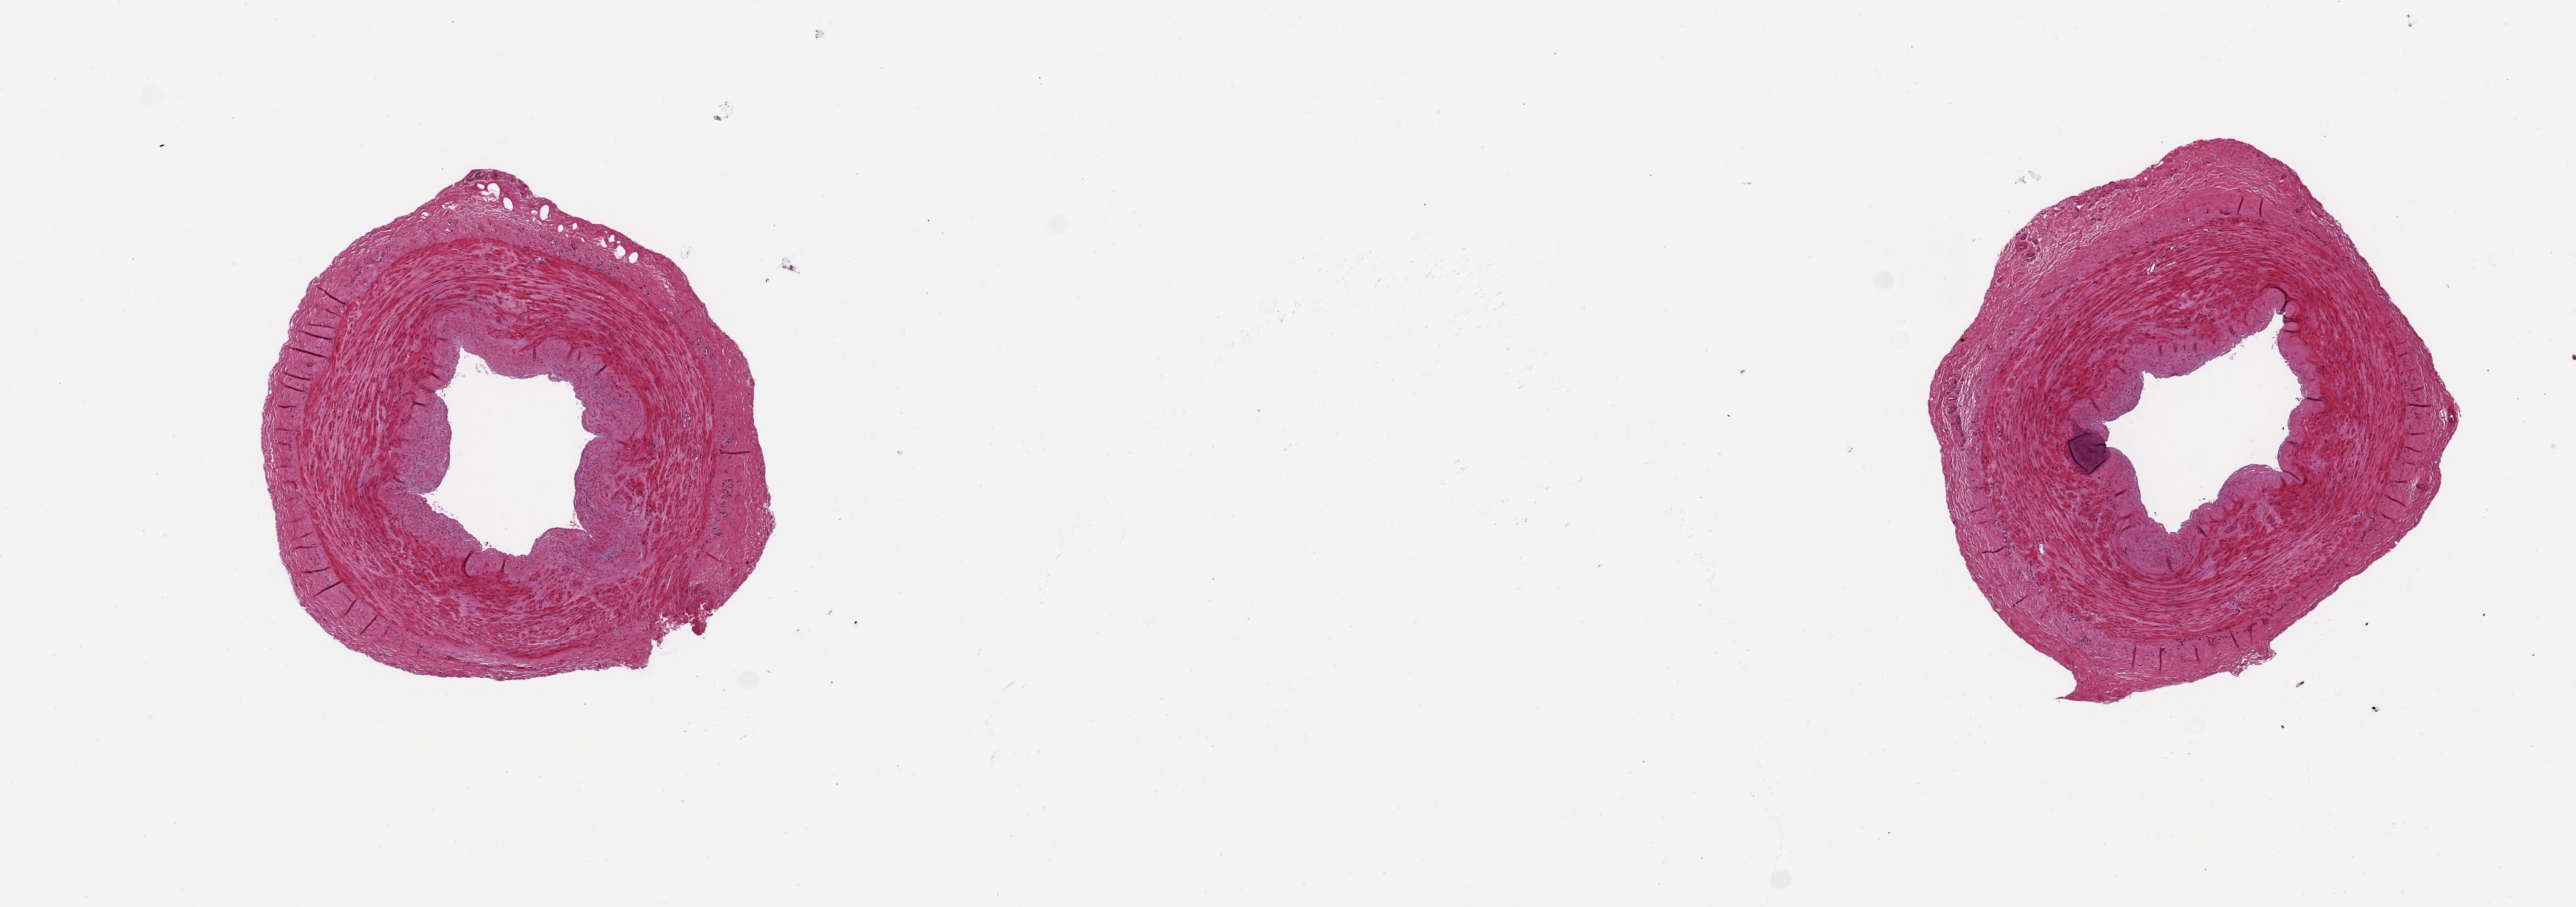
Digitized H&E-stained section, brightfield — a low-resolution overview of the entire scanned area, about 13.8 x 4.9 mm. PAXgene-fixed, paraffin-embedded tissue. Section of tibial artery (target tissue). Tissue donor sample. Male donor.
• pathologist's review note for this sample: 2 pieces 3x3 & 3x3mm; good clean specimens